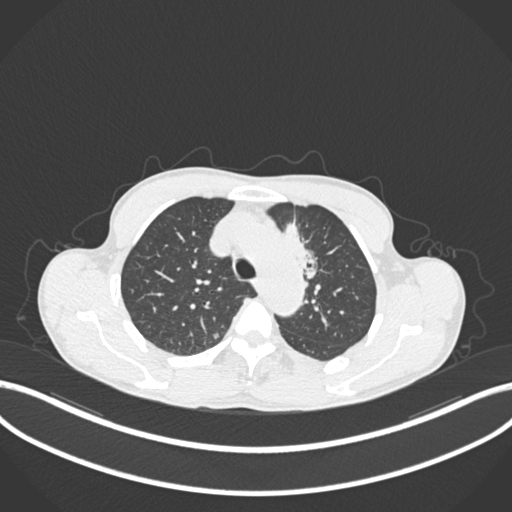
Chest CT, one axial slice. Position 152 of 211 along the scan axis. 120 kVp. Lung window (W 1500 / L -600 HU). 1 mm slice thickness. 512 × 512 image matrix. Patient: male, 58 years. Case-level facts recorded for this patient, not image findings: clinical TNM (as recorded): T1c N1 M0.
Annotated regions visible in this slice (rectangle marked by the reading radiologist):
- lung tumour (recorded histology: adenocarcinoma): bounding box [x1, y1, x2, y2] px = [280, 220, 322, 280]